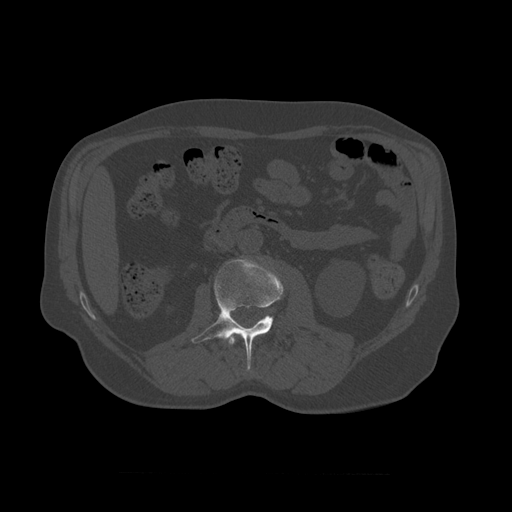
CT including the spine, one axial slice; position 328 of 450 along the scan axis; reconstruction kernel STANDARD; 120 kVp; bone window (W 1800 / L 400 HU); 1.25 mm slice thickness; 512 × 512 image matrix, field of view 405 × 405 mm. Patient age 75 years. Case-level facts recorded for this patient, not image findings: primary cancer: prostate.
Structures marked on this image (semi-automatic segmentation, software-assisted and operator-edited):
- L1 vertebra: bounding box <229,336,236,346> (left, top, right, bottom; pixels)
- L2 vertebra: <192,257,284,371>